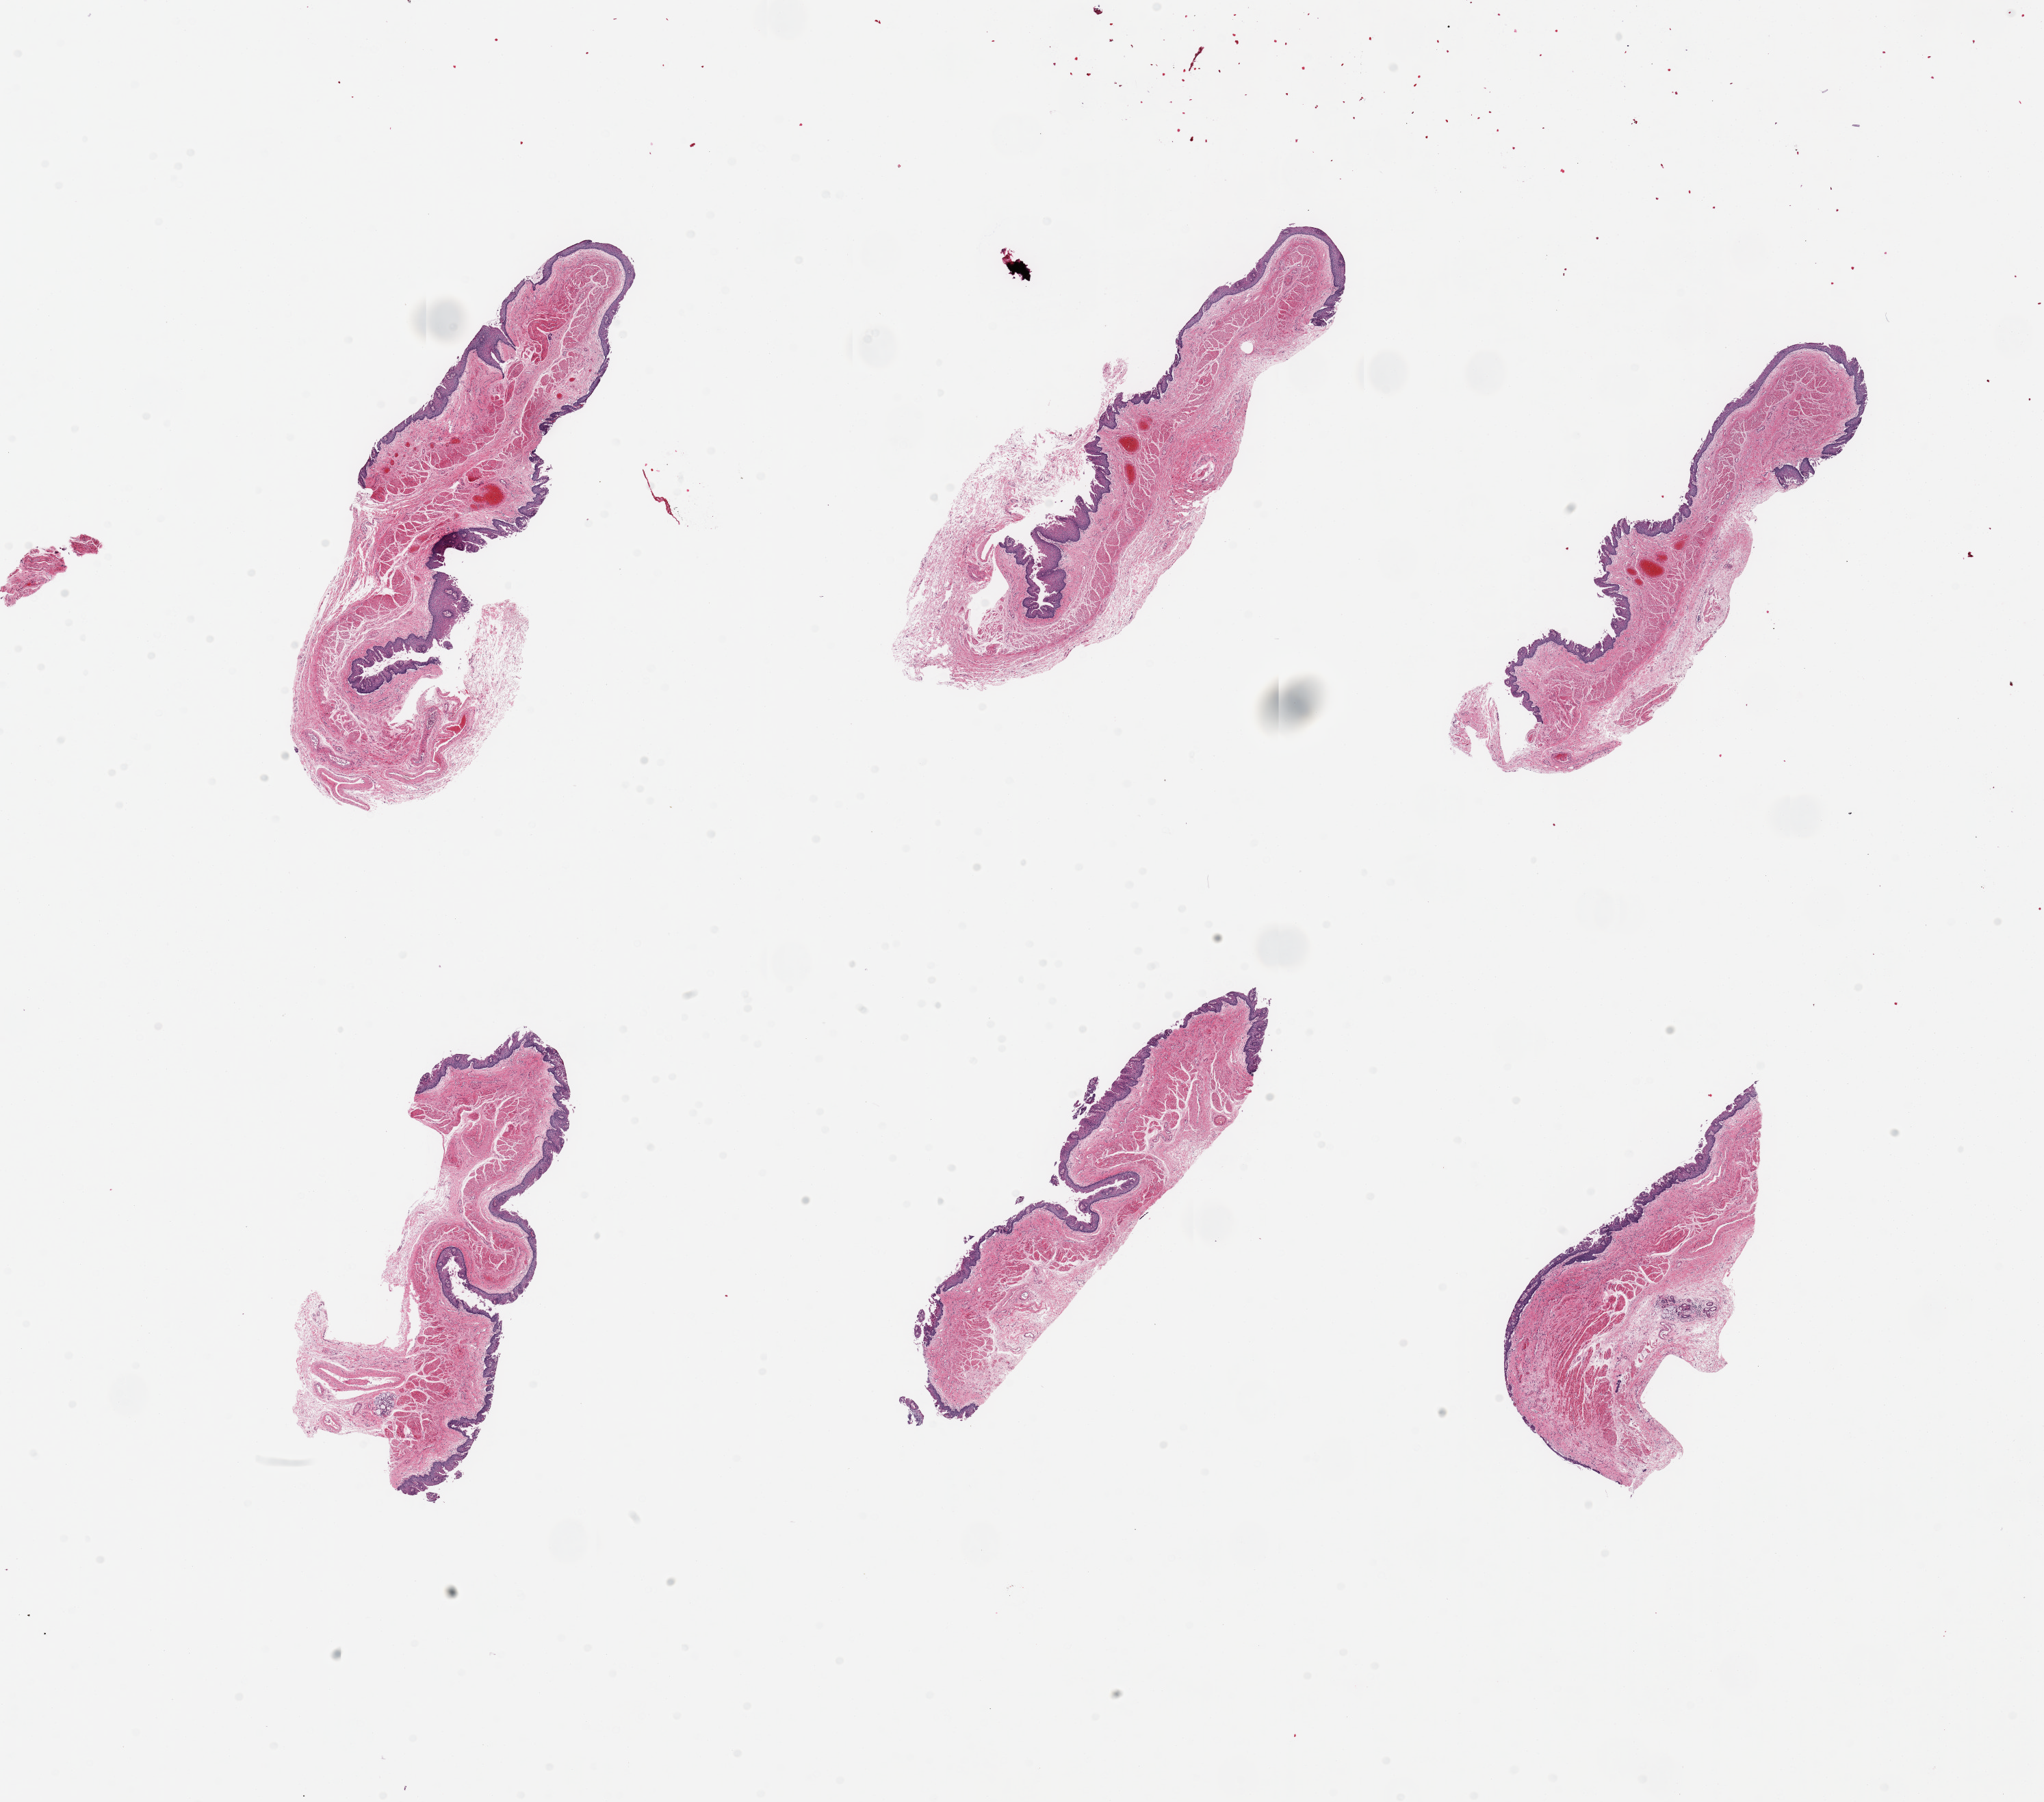
Digitized hematoxylin and eosin (H&E)-stained section, a low-resolution overview of the entire scanned area, about 23.6 x 20.8 mm. PAXgene-fixed, paraffin-embedded tissue. Section of esophageal mucous membrane (target tissue). Donor tissue sample. Male donor.
Reviewer comment on this tissue sample: 6 pieces; epithelium partially sloughed.